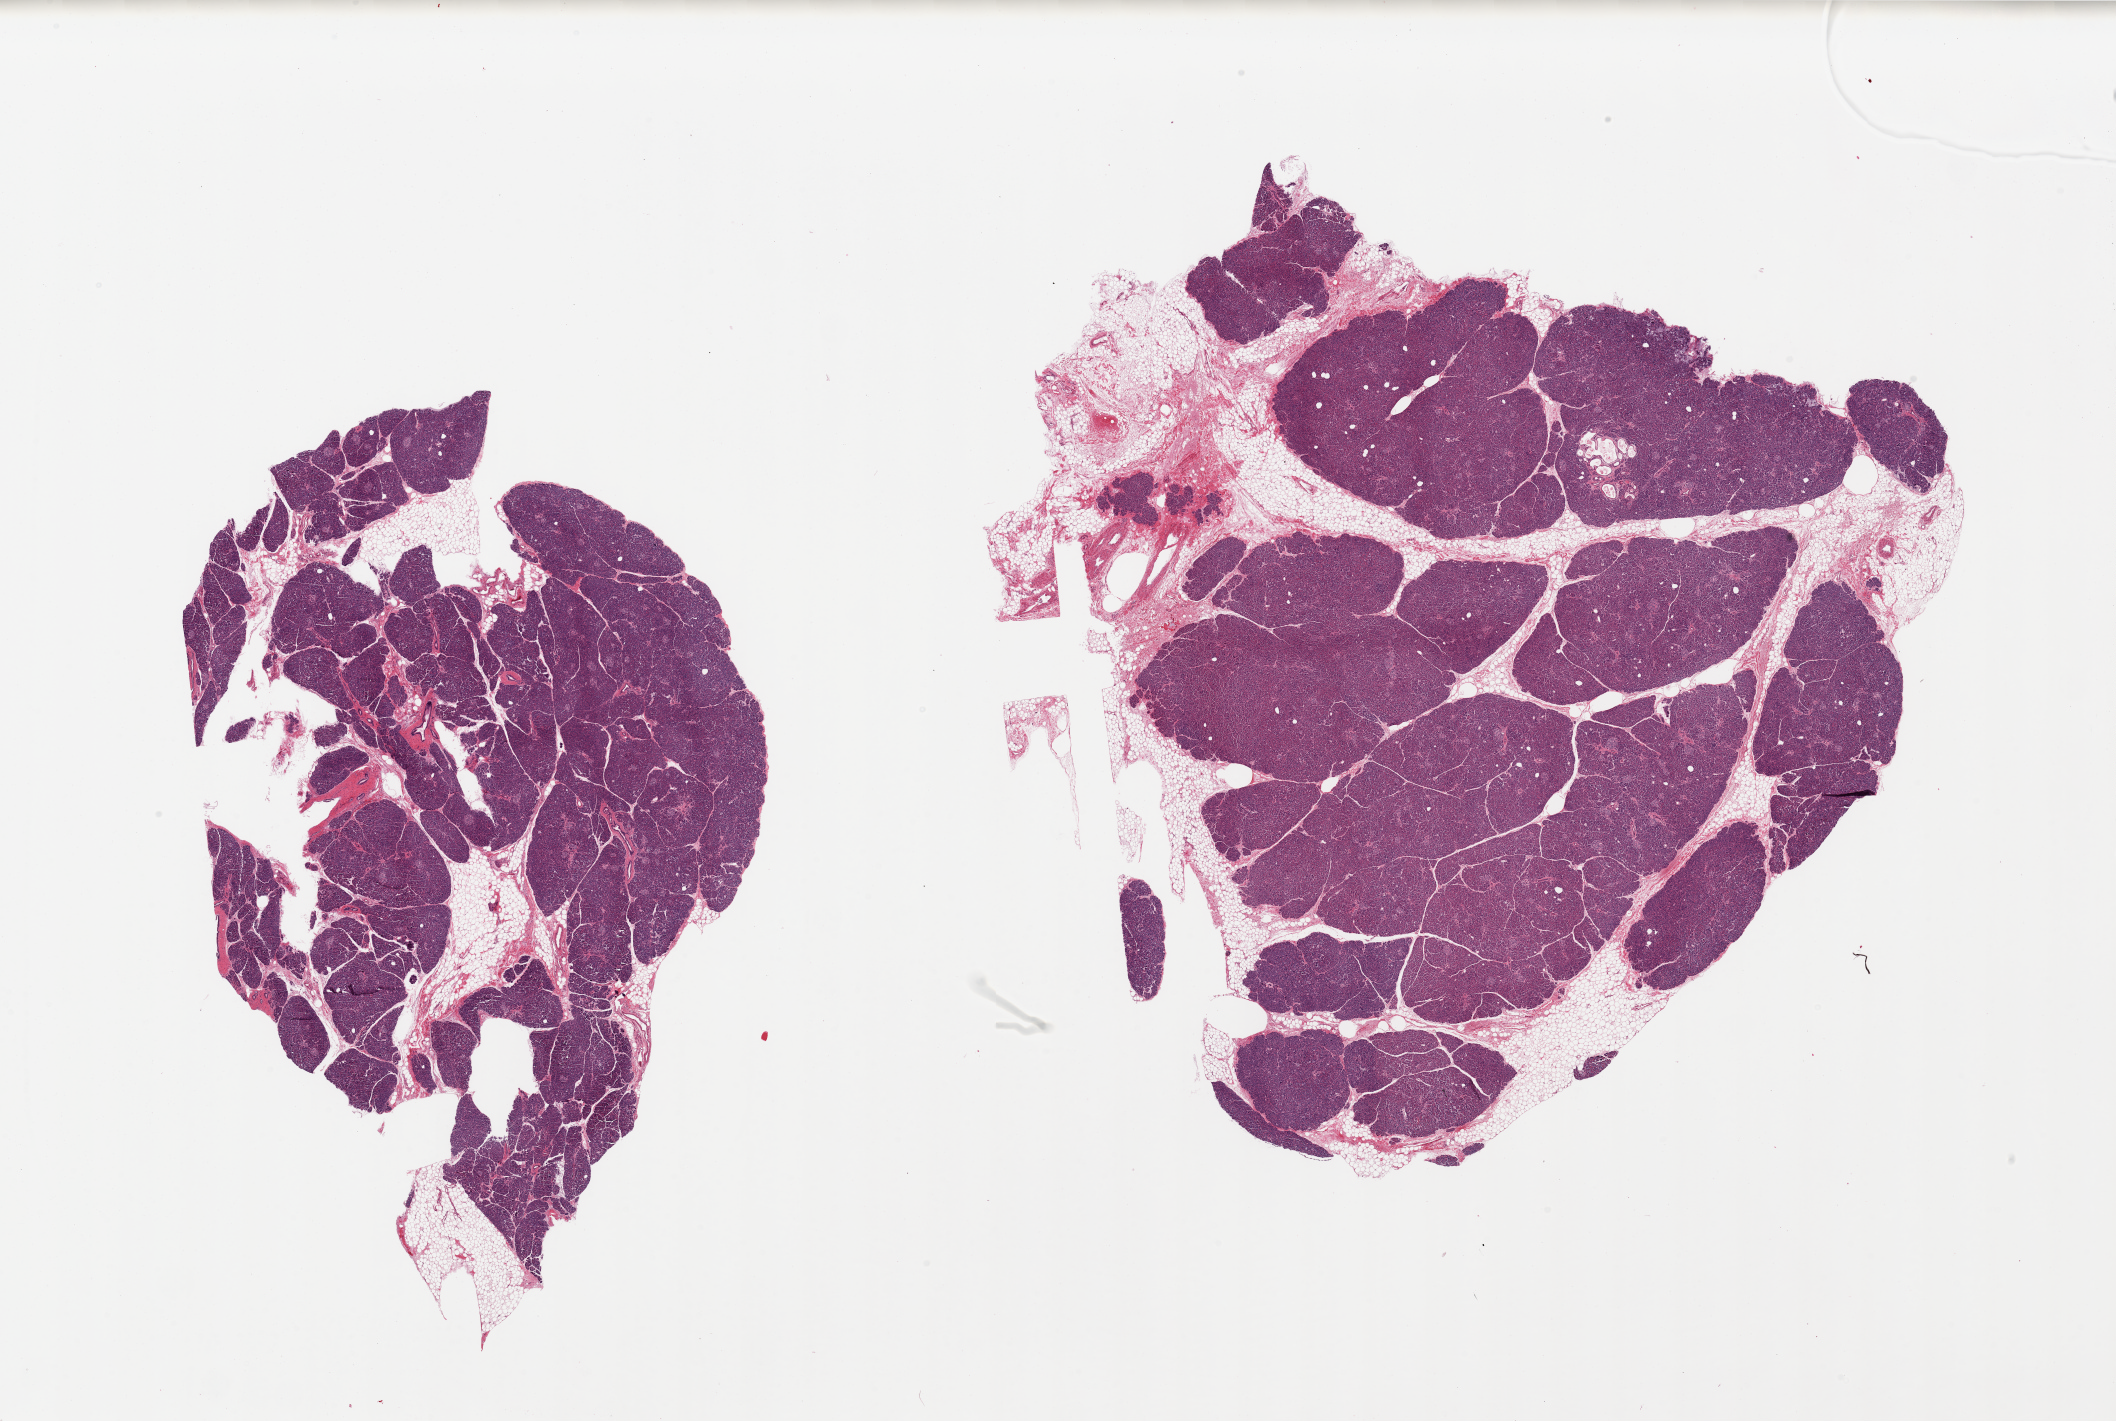
Digitized hematoxylin and eosin (H&E)-stained section — shown as a low-resolution overview of the whole scanned area (about 33.5 x 22.5 mm, acquisition: 20x scan). PAXgene-fixed, paraffin-embedded tissue. Sampled site (target tissue): pancreas. Tissue donor sample.
* reviewer comment on this tissue sample: 2 pieces, reasonably well preserved, 1-2, islets well-visualized